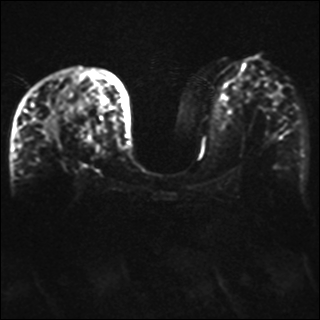
Breast MRI, one axial slice. Slice 18 of 42 in the series (ordered by position). Diffusion-weighted series; image 2 of 4 stored at this slice position (different b-values; order by instance number). 1.5 T. 320 × 320 image matrix, field of view 330 × 330 mm. Female patient.
Annotated regions visible in this slice (manually delineated by an expert):
- tumour on diffusion-weighted imaging: bounding box <43,119,54,141> (left, top, right, bottom; pixels)